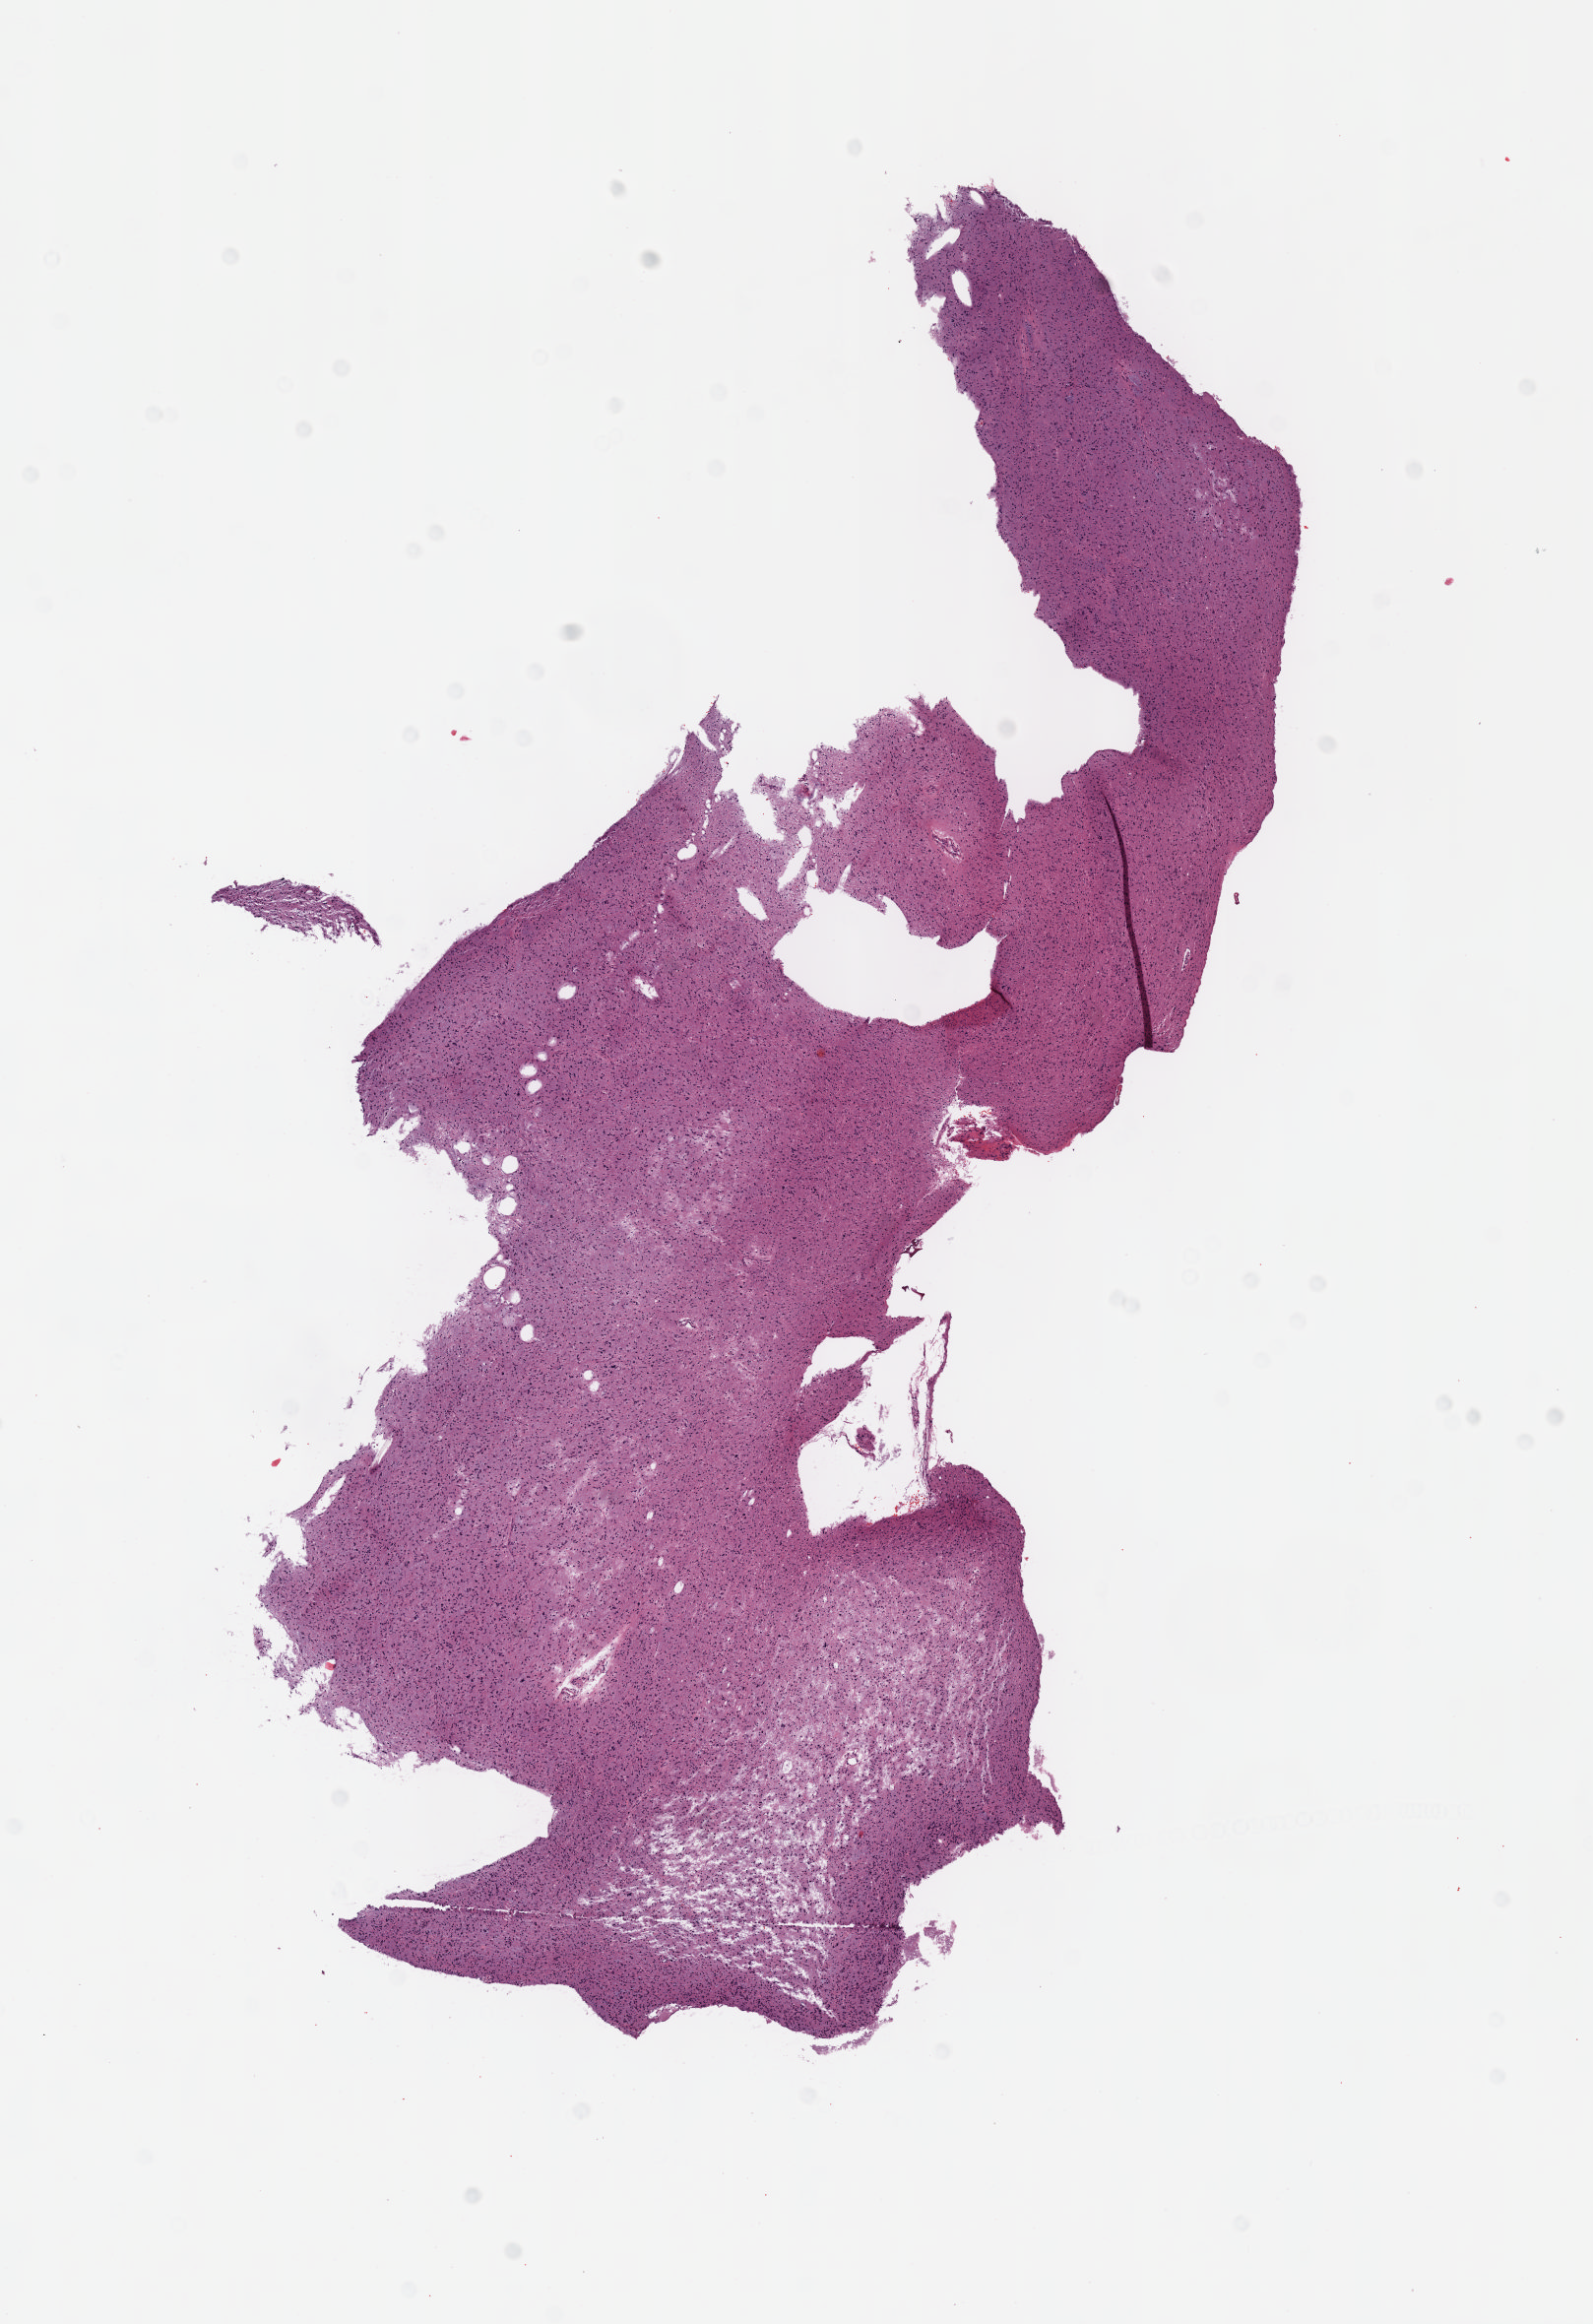
Digitized Hematoxylin and eosin (H&E) stained tissue section (whole slide), a low-resolution overview of the entire scanned area, about 6.5 x 9.5 mm, formalin-fixed paraffin-embedded (FFPE) diagnostic section, sample: primary tumour, brain. Female, age 18 years at initial diagnosis. Histologic grade: G2 (moderately differentiated).
Pathologic diagnosis: Mixed glioma. Laterality: left.